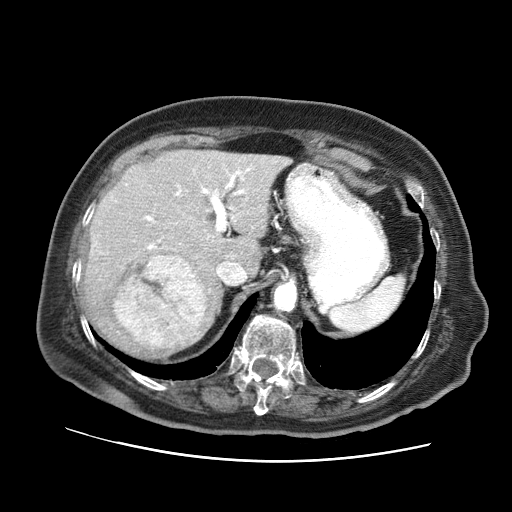
Contrast-enhanced abdominal CT (liver protocol), one axial slice. Reconstruction kernel STANDARD. Soft-tissue window (W 400 / L 40 HU). 512 × 512 image matrix, field of view 380 × 380 mm. From the clinical record (not read from this slice): diagnosis: hepatocellular carcinoma (patient treated with transarterial chemoembolisation; whether this scan precedes or follows treatment is not stated here); TNM stage (as recorded): Stage-I; Child-Pugh class: A; tumour differentiation: well differentiated; tumour nodularity: uninodular.
Structures marked on this image (semi-automatically segmented with operator editing):
- liver parenchyma outside the tumour (the mass and vessels are separate outlines, so this box may not span the whole liver): bounding box (x1, y1, x2, y2) in pixels: (84, 150, 289, 360)
- mass: (114, 255, 206, 347)
- liver vessels: (144, 168, 250, 250)